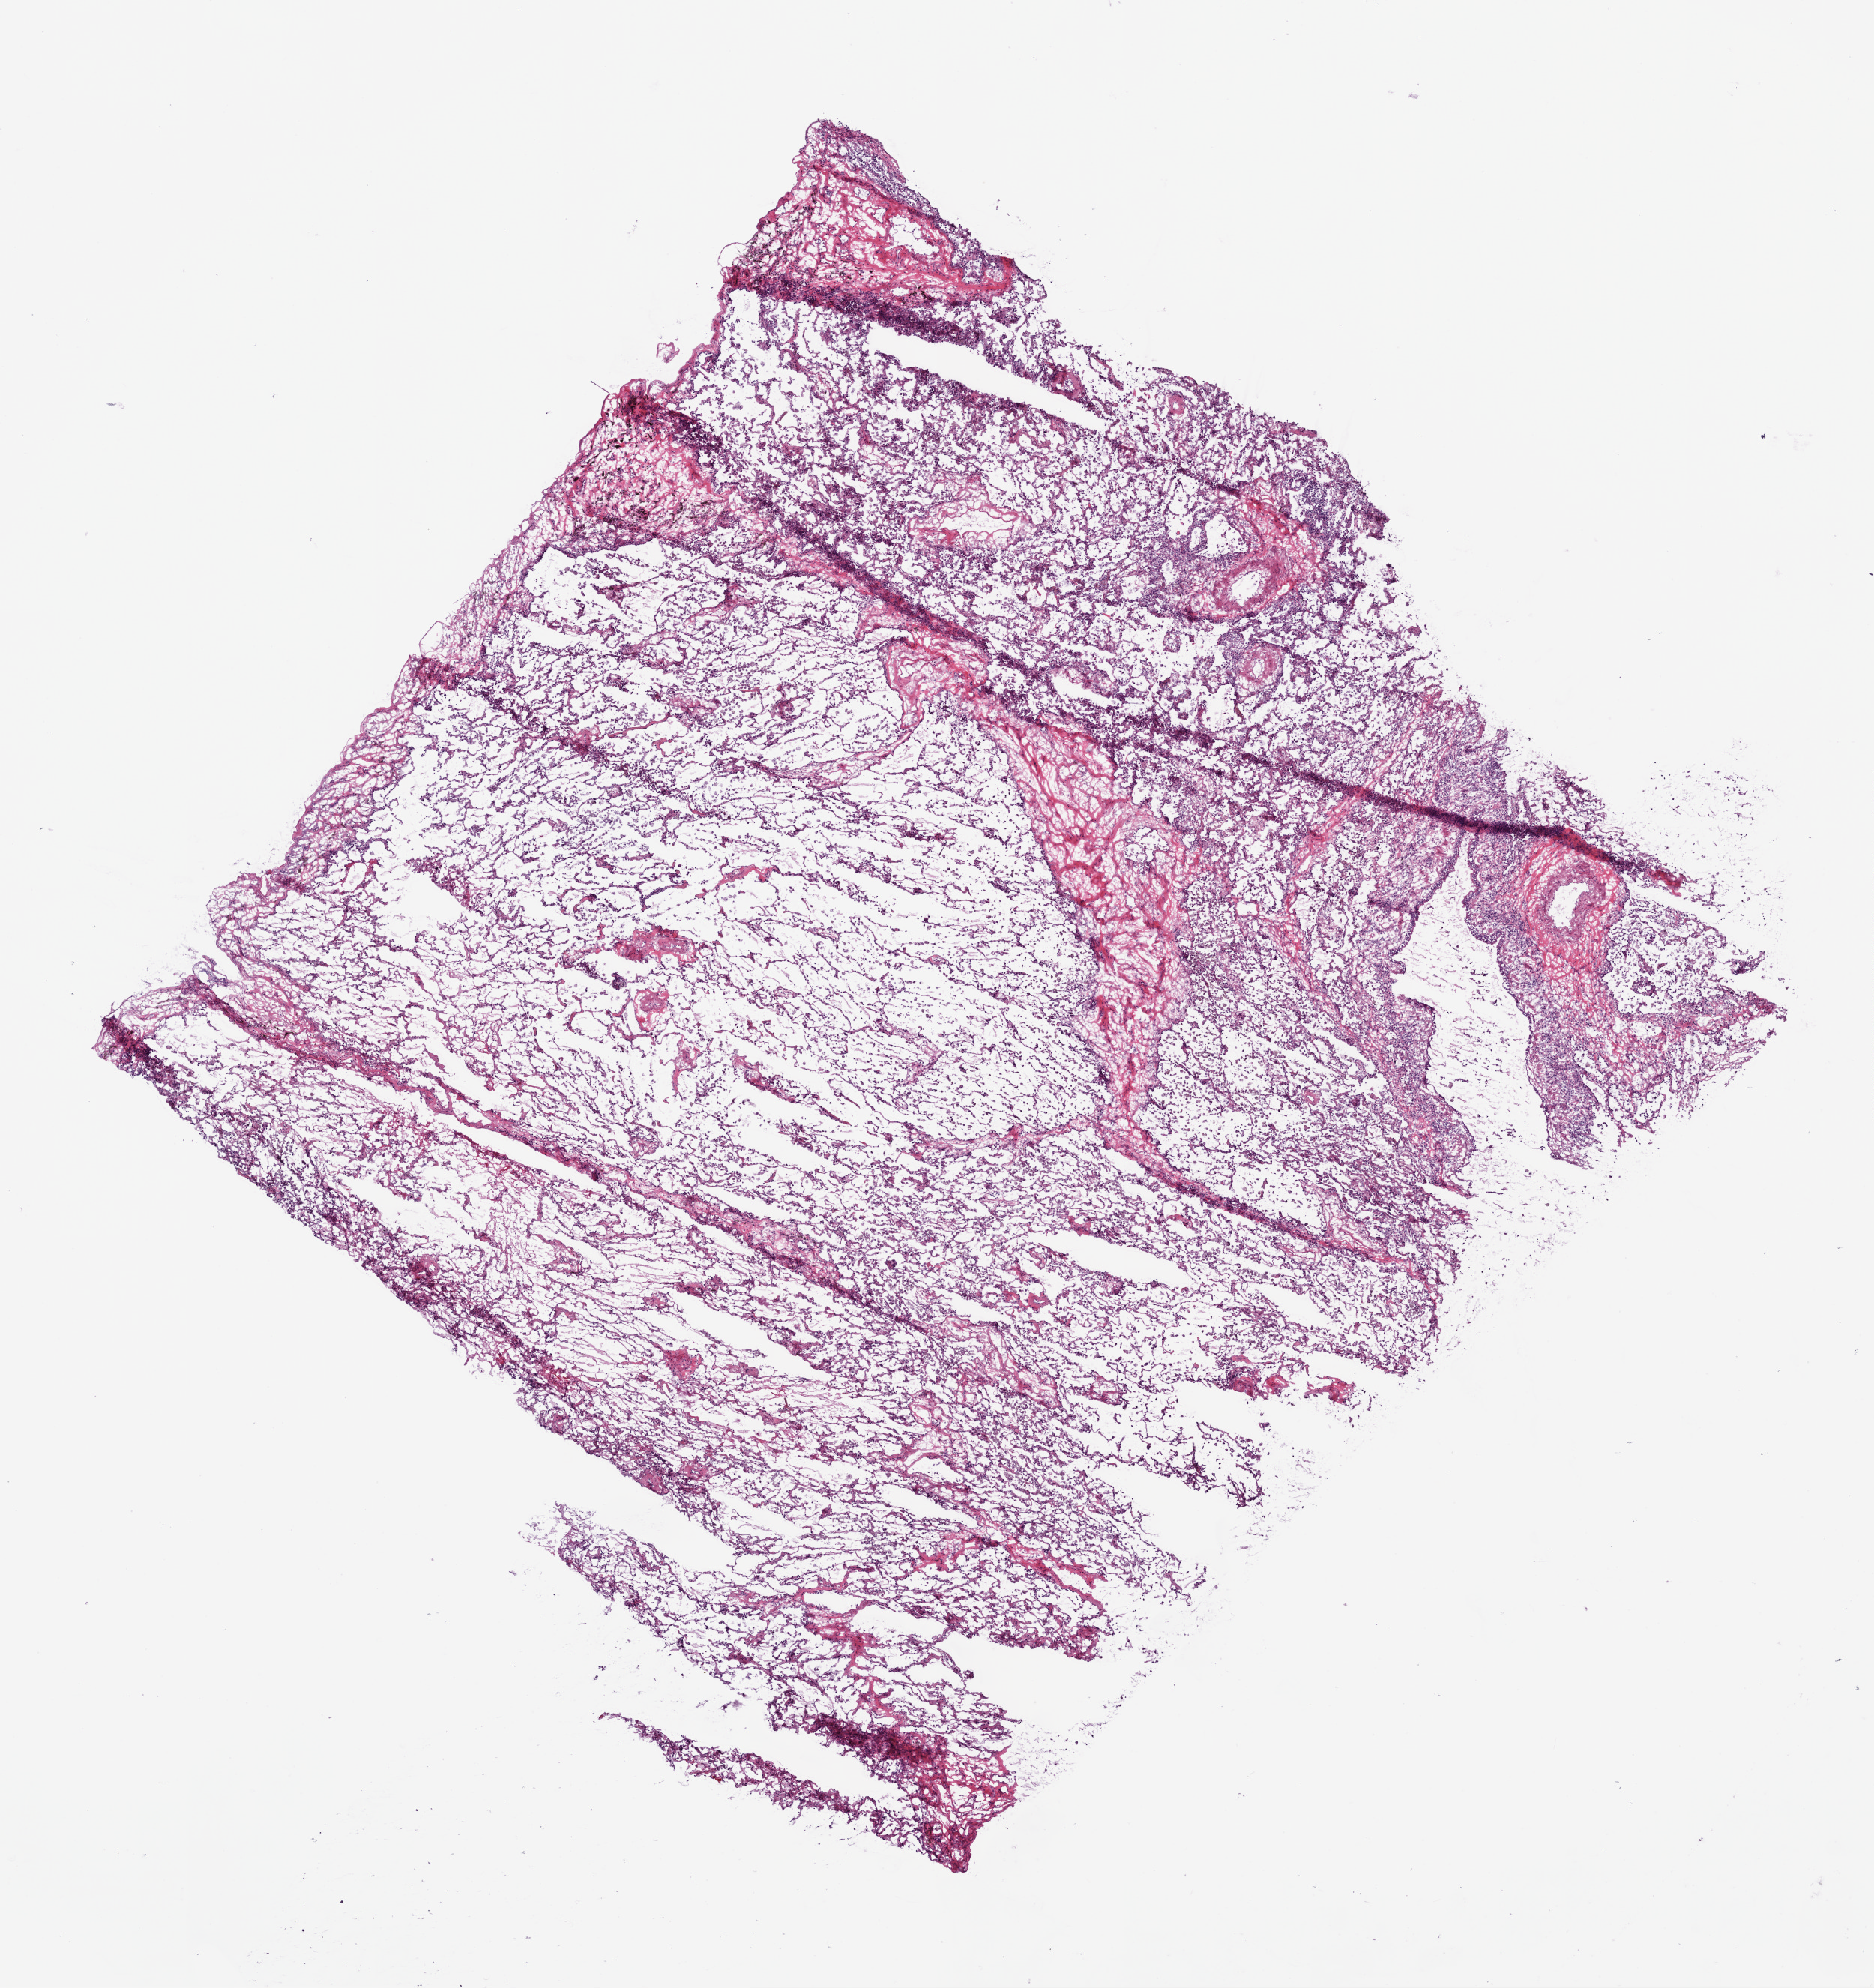
Digitized H&E tissue section (whole slide), low-resolution overview of the scanned area, about 10.0 x 10.6 mm; frozen section; sample: solid tissue normal (non-tumour tissue), lung. Male patient; age at initial diagnosis 55 years.
This section: solid tissue normal (non-tumour) sample from the same patient. Patient diagnosis: Squamous cell carcinoma, NOS (upper lobe, lung).